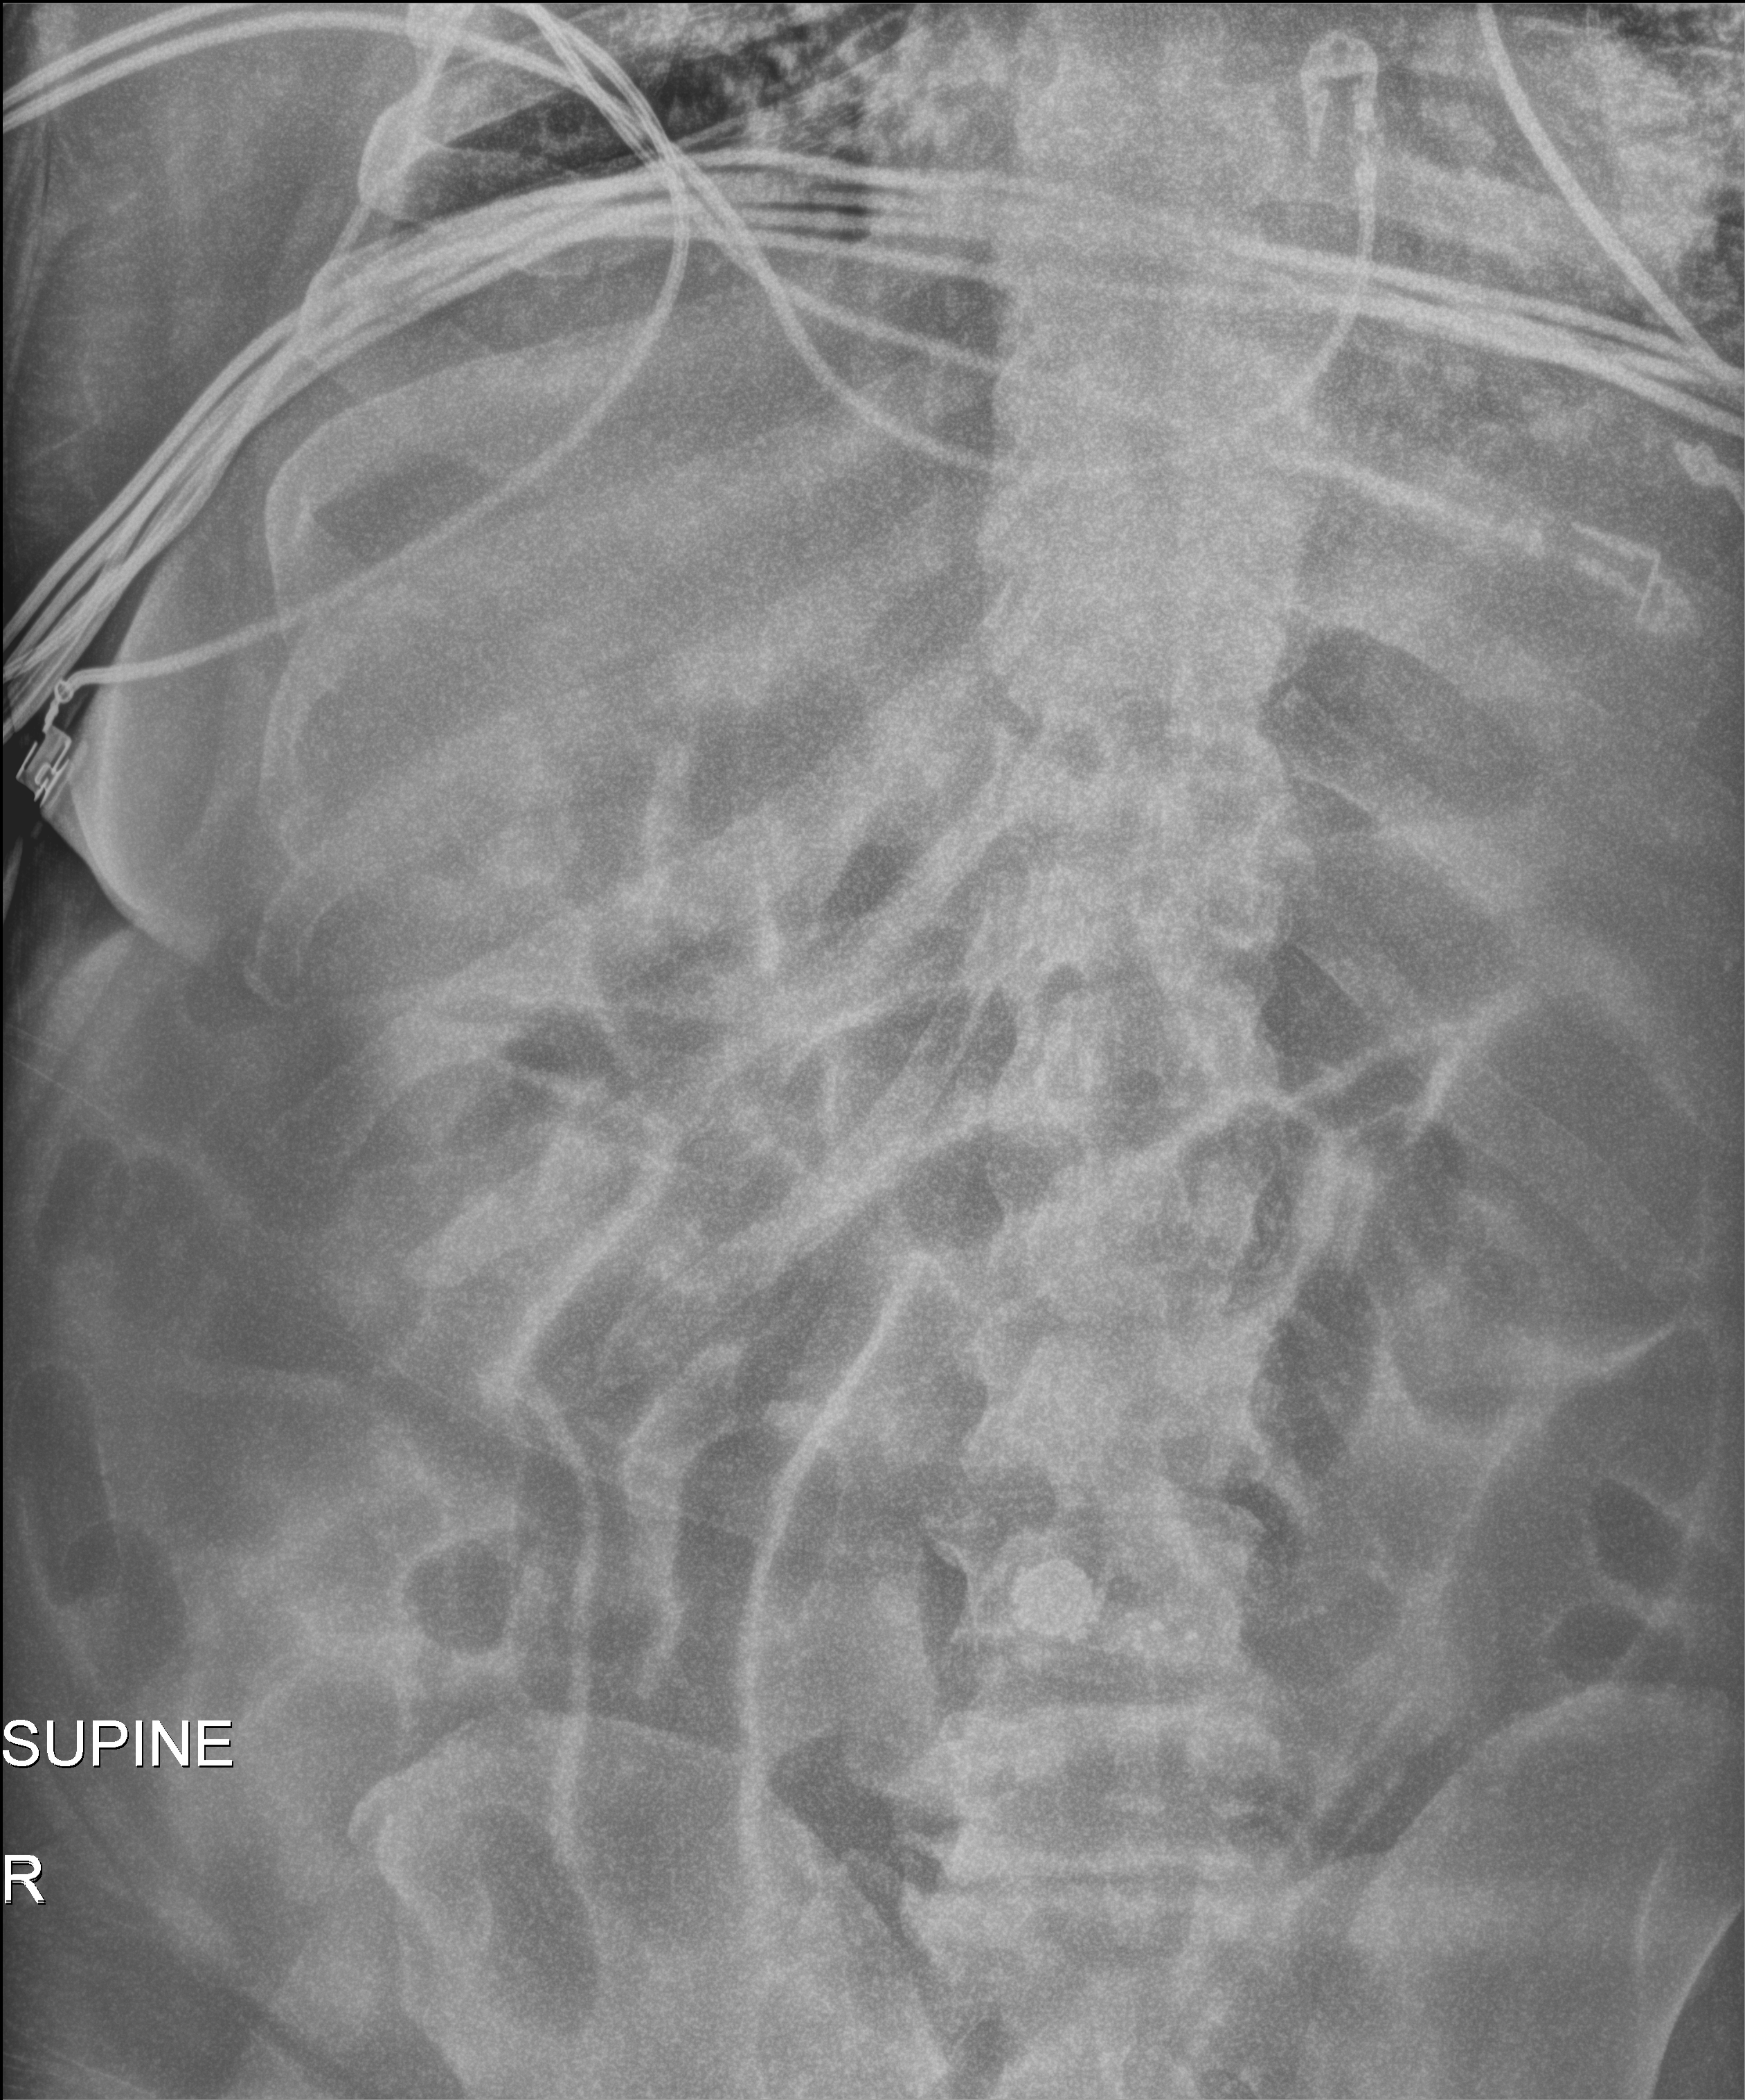
Bedside abdomen radiograph (digital radiography), anteroposterior (AP) projection. Patient hospitalised with COVID-19; male, aged 18–59 years.
Hospital-stay facts (about this admission, not read from this image; timing relative to this image not recorded):
- diabetes (admission record): no
- mechanically ventilated during this hospital stay: yes
- admitted to intensive care during this hospital stay: yes